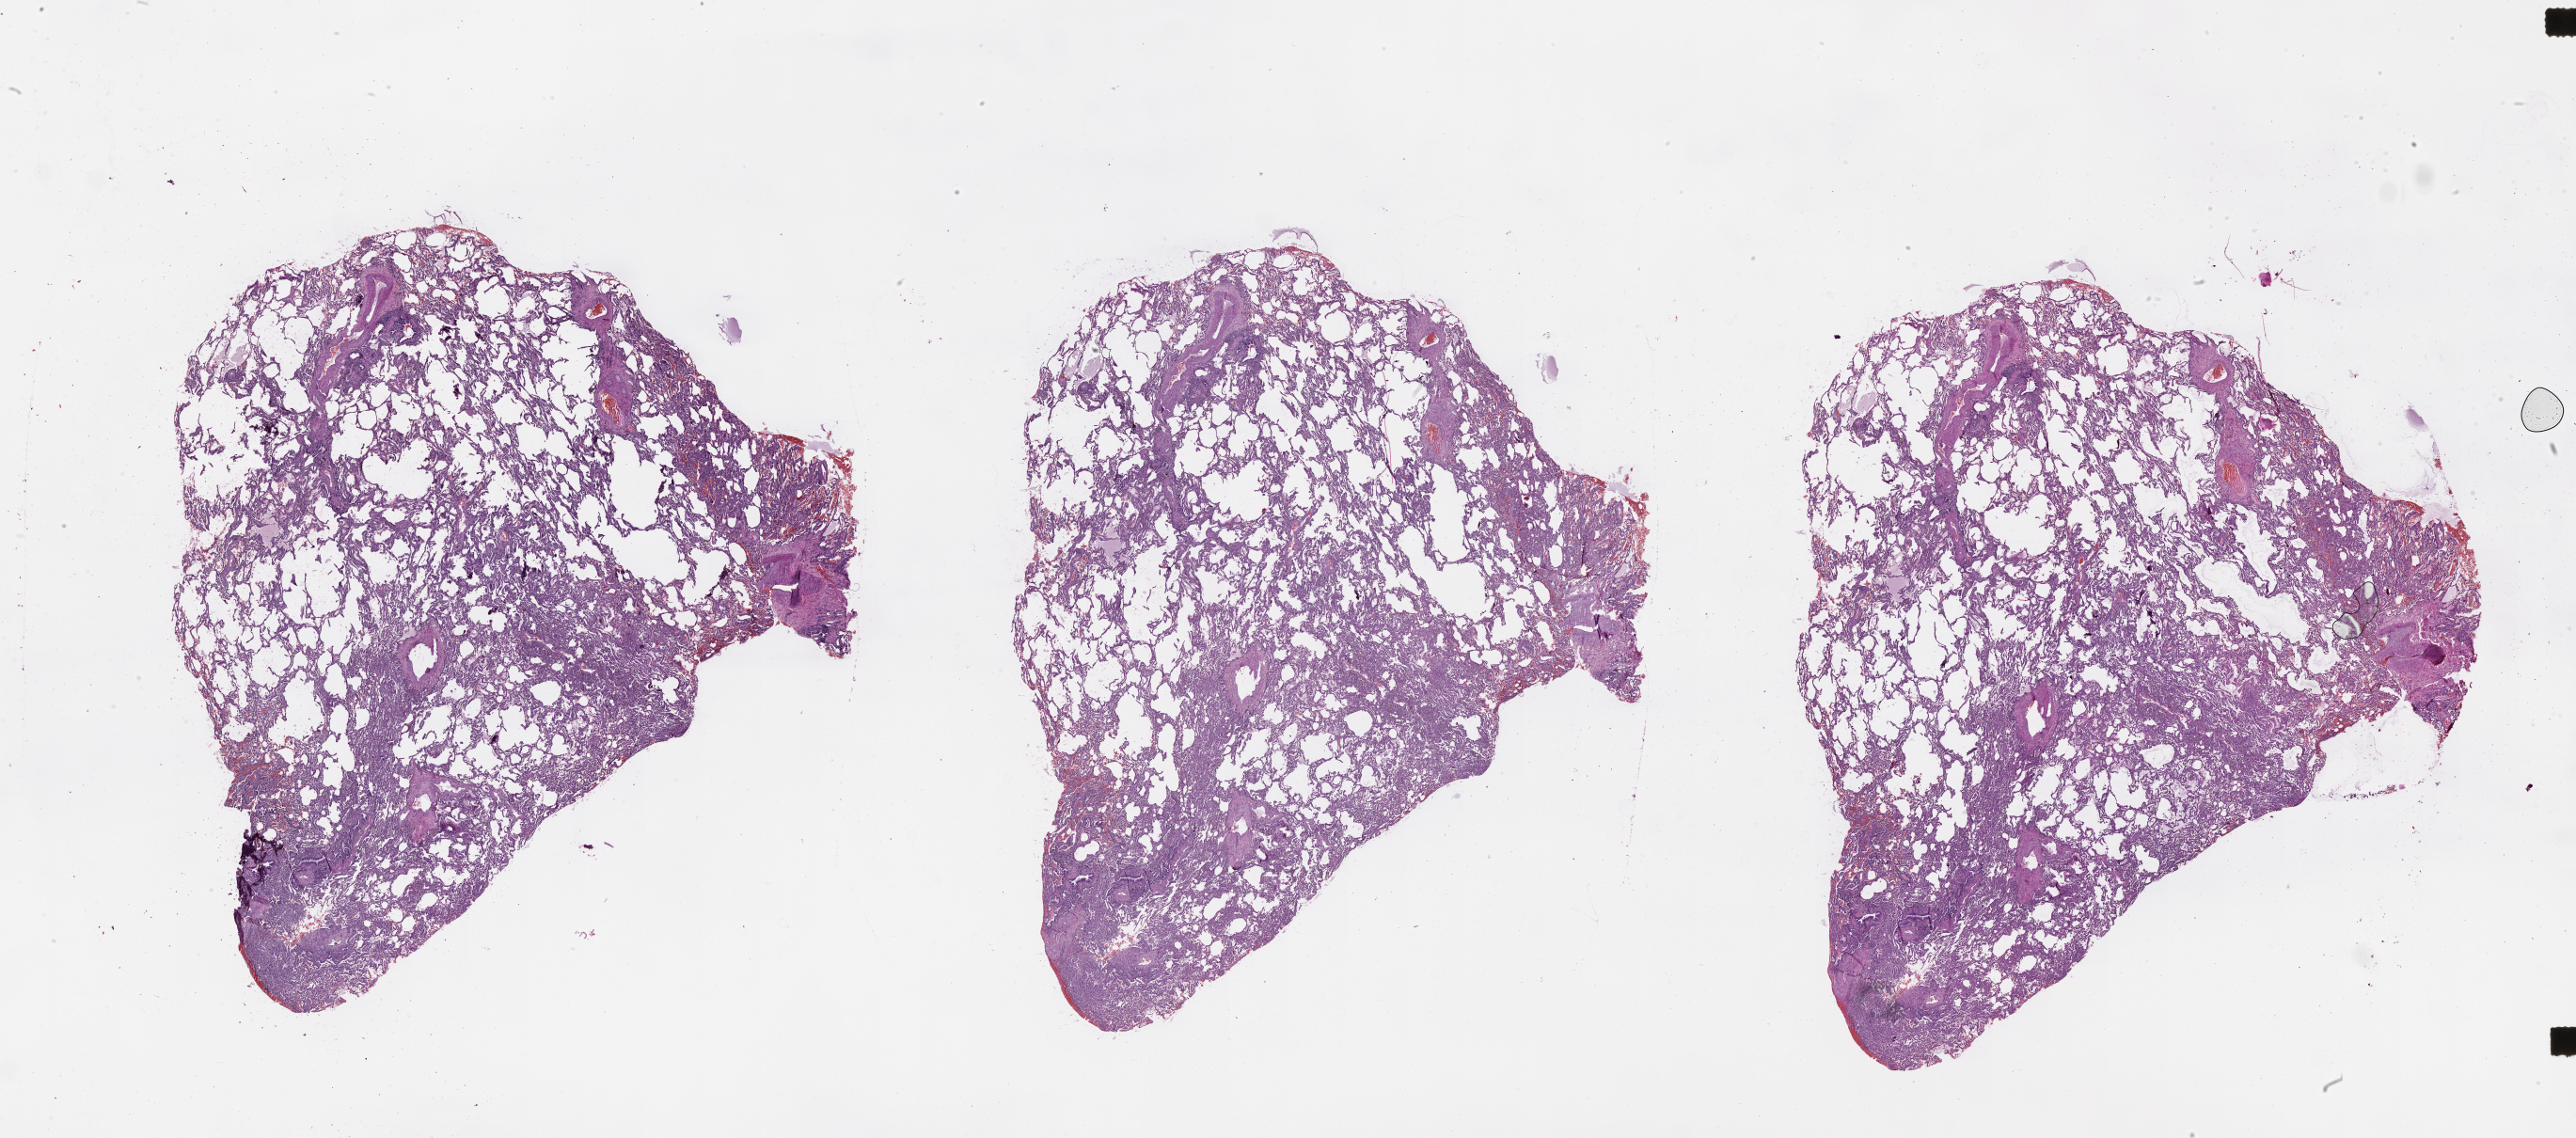
Whole-slide histology image, H&E, whole scanned area (about 44.1 x 19.5 mm) shown as a low-resolution overview, lung, normal (non-tumour) tissue. Male, 49 y/o.
This section: normal (non-tumour) tissue from the same patient. Patient diagnosis (cohort enrolment): squamous cell carcinoma (lung).